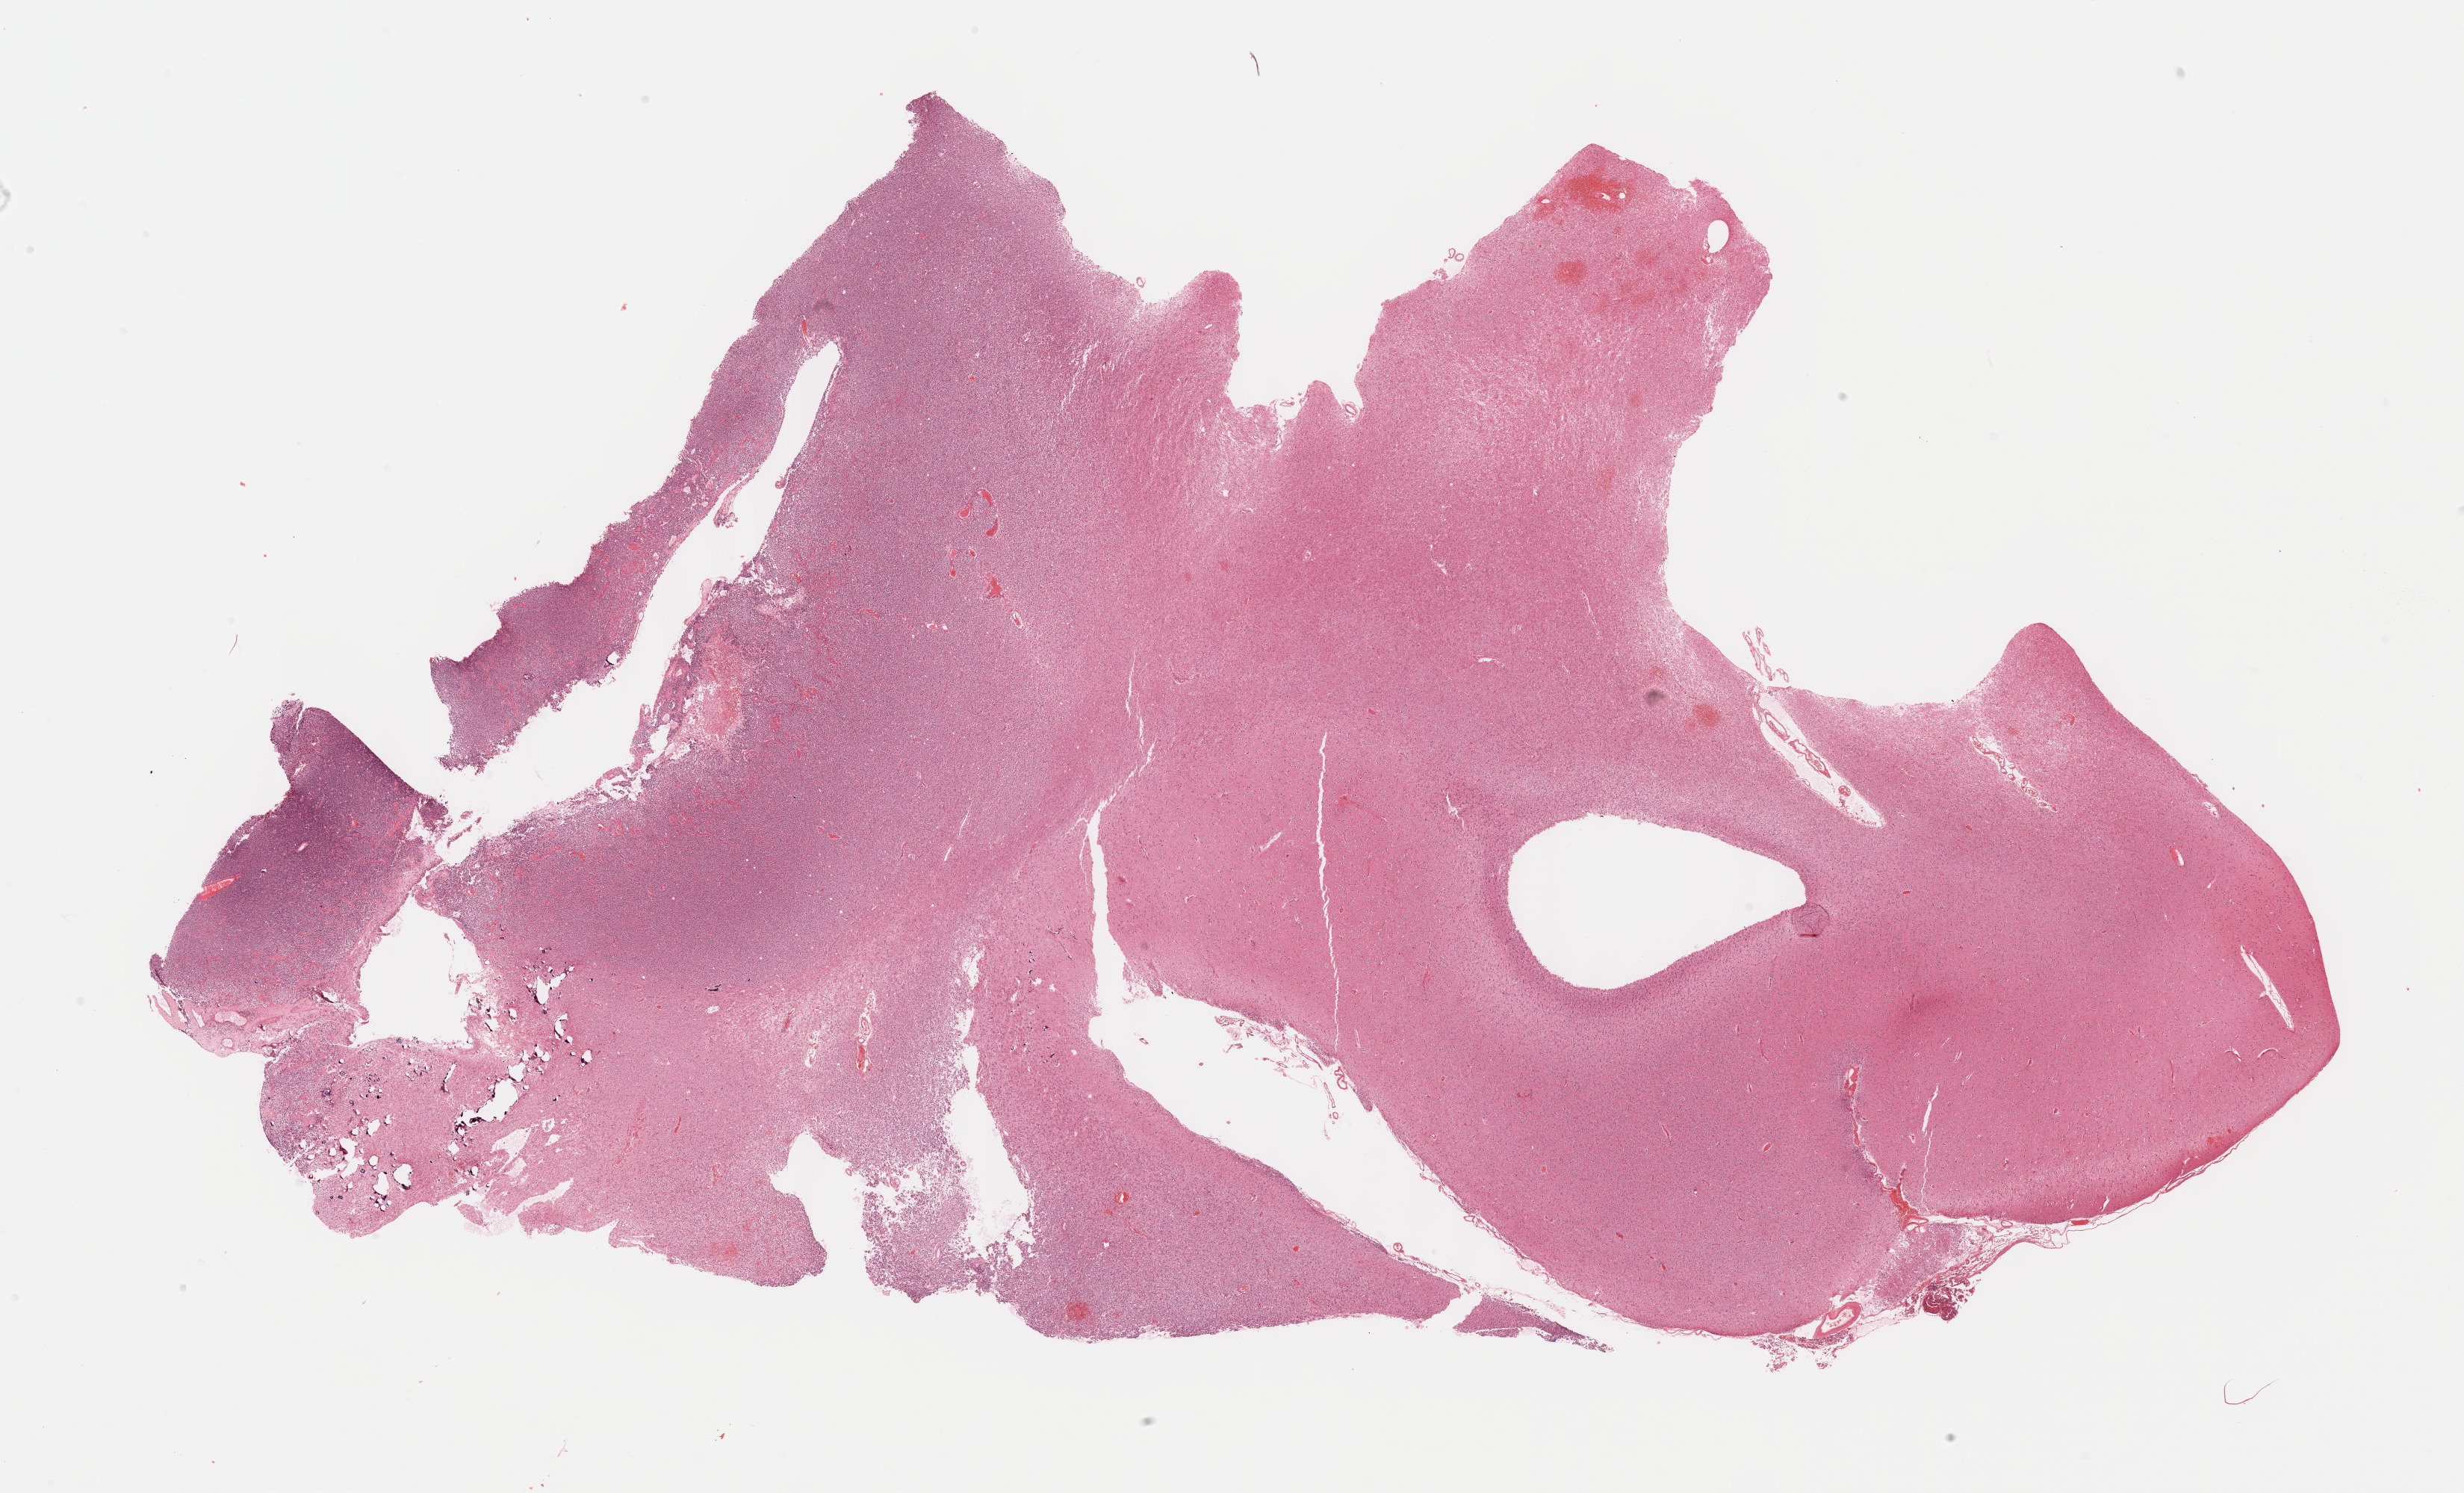
Whole-slide histology image, H&E, low-resolution overview of the scanned area, about 26.7 x 16.2 mm (acquisition: 40x scan); formalin-fixed paraffin-embedded (FFPE) diagnostic section; primary tumour sample from the brain. Female patient; age at initial diagnosis 54 years. Histologic grade: G3 (poorly differentiated).
Diagnosis: Oligodendroglioma, anaplastic (cerebrum).